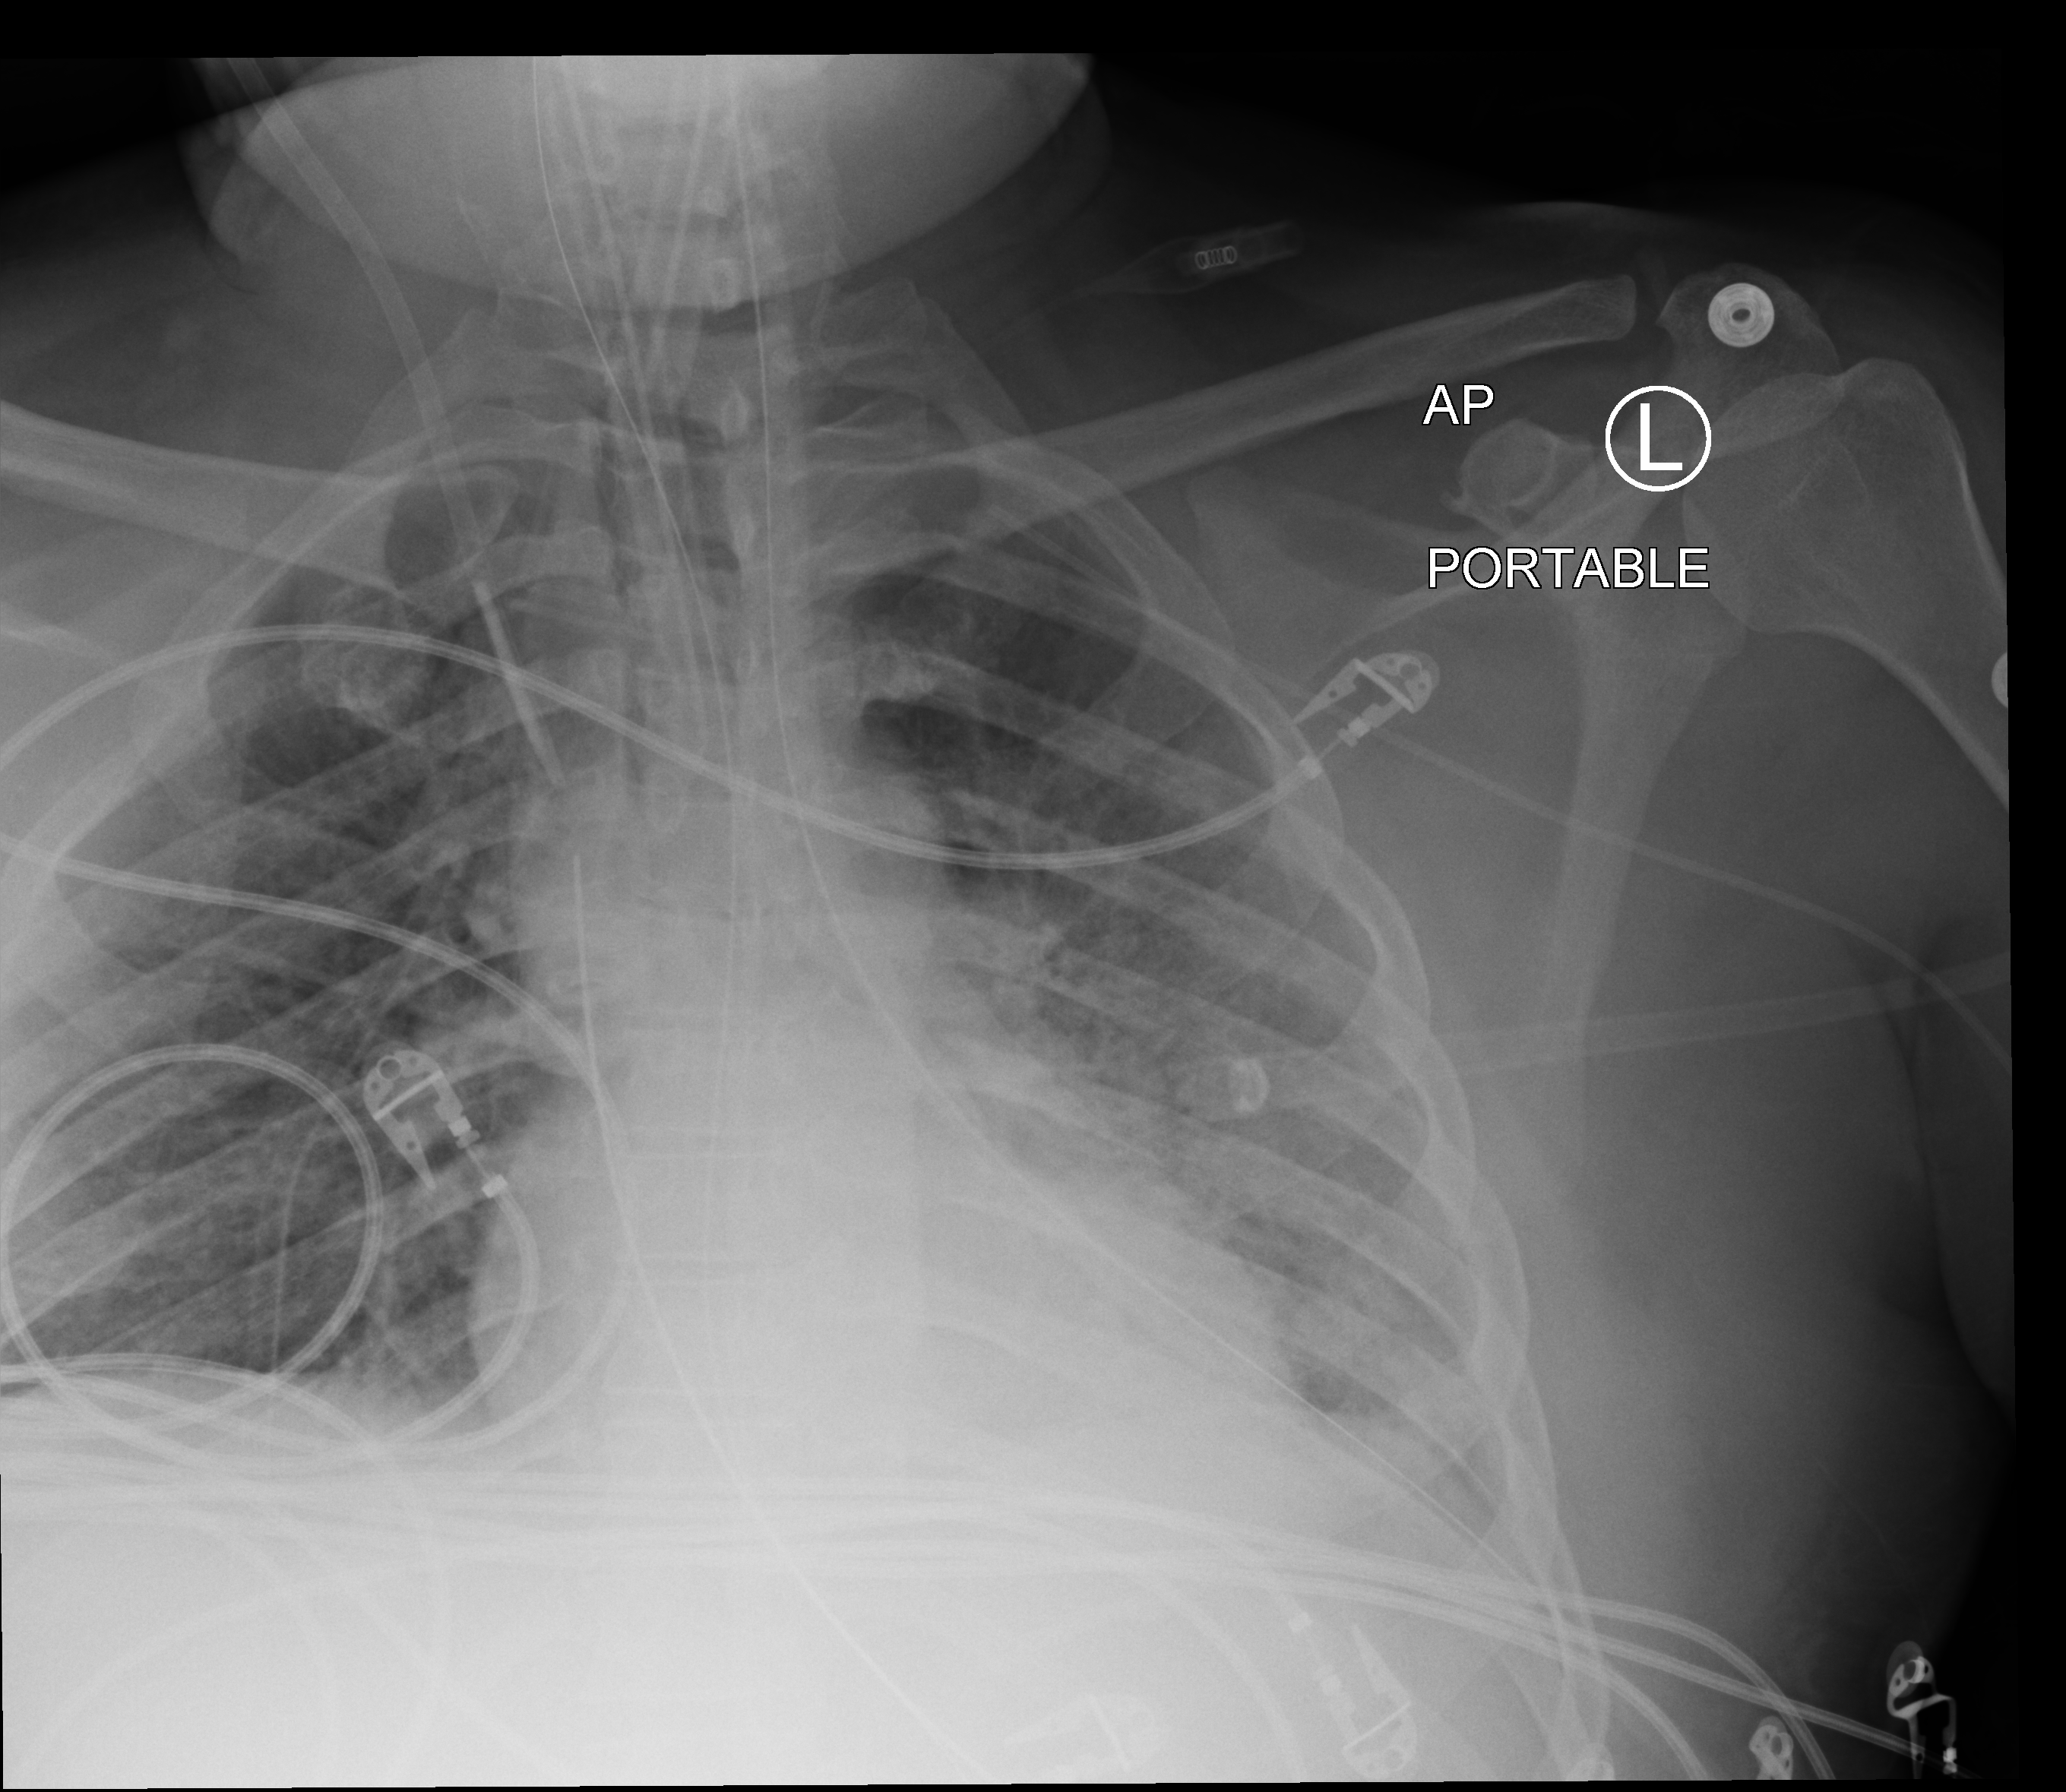
Chest X-ray (portable). Adult patient hospitalised with COVID-19, age 18–59 years.
Admission-level facts for this patient (not findings on this image; timing relative to this image not recorded):
- admitted to intensive care during this hospital stay: yes
- mechanically ventilated during this hospital stay: yes